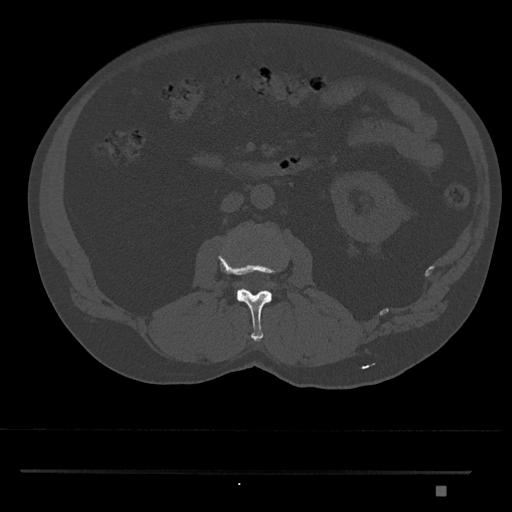
CT including the spine, one axial slice; reconstruction kernel Br40s/3; bone window (W 1800 / L 400 HU); 0.5 mm slice thickness; 512 × 512 image matrix, field of view 429 × 429 mm. Patient: male, 65 years. From the clinical record (not read from this slice): primary cancer: prostate.
Outlined on this slice (semi-automatically segmented with operator editing):
- L2 vertebra: bounding box [x1, y1, x2, y2] px = [219, 252, 282, 342]
- L3 vertebra: [272, 283, 275, 285]